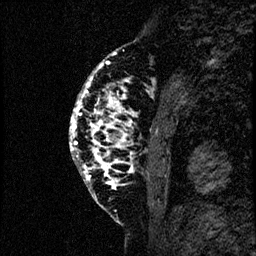
Breast MRI (dynamic contrast-enhanced), one sagittal slice; position 21 of 60 along the scan axis; dynamic contrast-enhanced study with each time point stored as its own series, time point 2 of 4 at this slice position (early post-contrast, ordered by acquisition time); 1.5 T; TE 4.2 ms, TR 17.6 ms; 2 mm slice thickness; 256 × 256 image matrix. Female patient, age 40 years. From the clinical record (not read from this slice): setting: breast cancer imaged before/during neoadjuvant chemotherapy; receptor status: HER2-positive.
Outlined on this slice (semi-automatic segmentation, software-assisted and operator-edited):
- analysis volume of interest (the breast-tissue region the enhancement analysis was run in; not a lesion): bounding box [x1, y1, x2, y2] px = [66, 55, 181, 206]
- tumour enhancement mask (voxels above the 100 % enhancement threshold inside the analysis volume of interest): [69, 63, 129, 185]